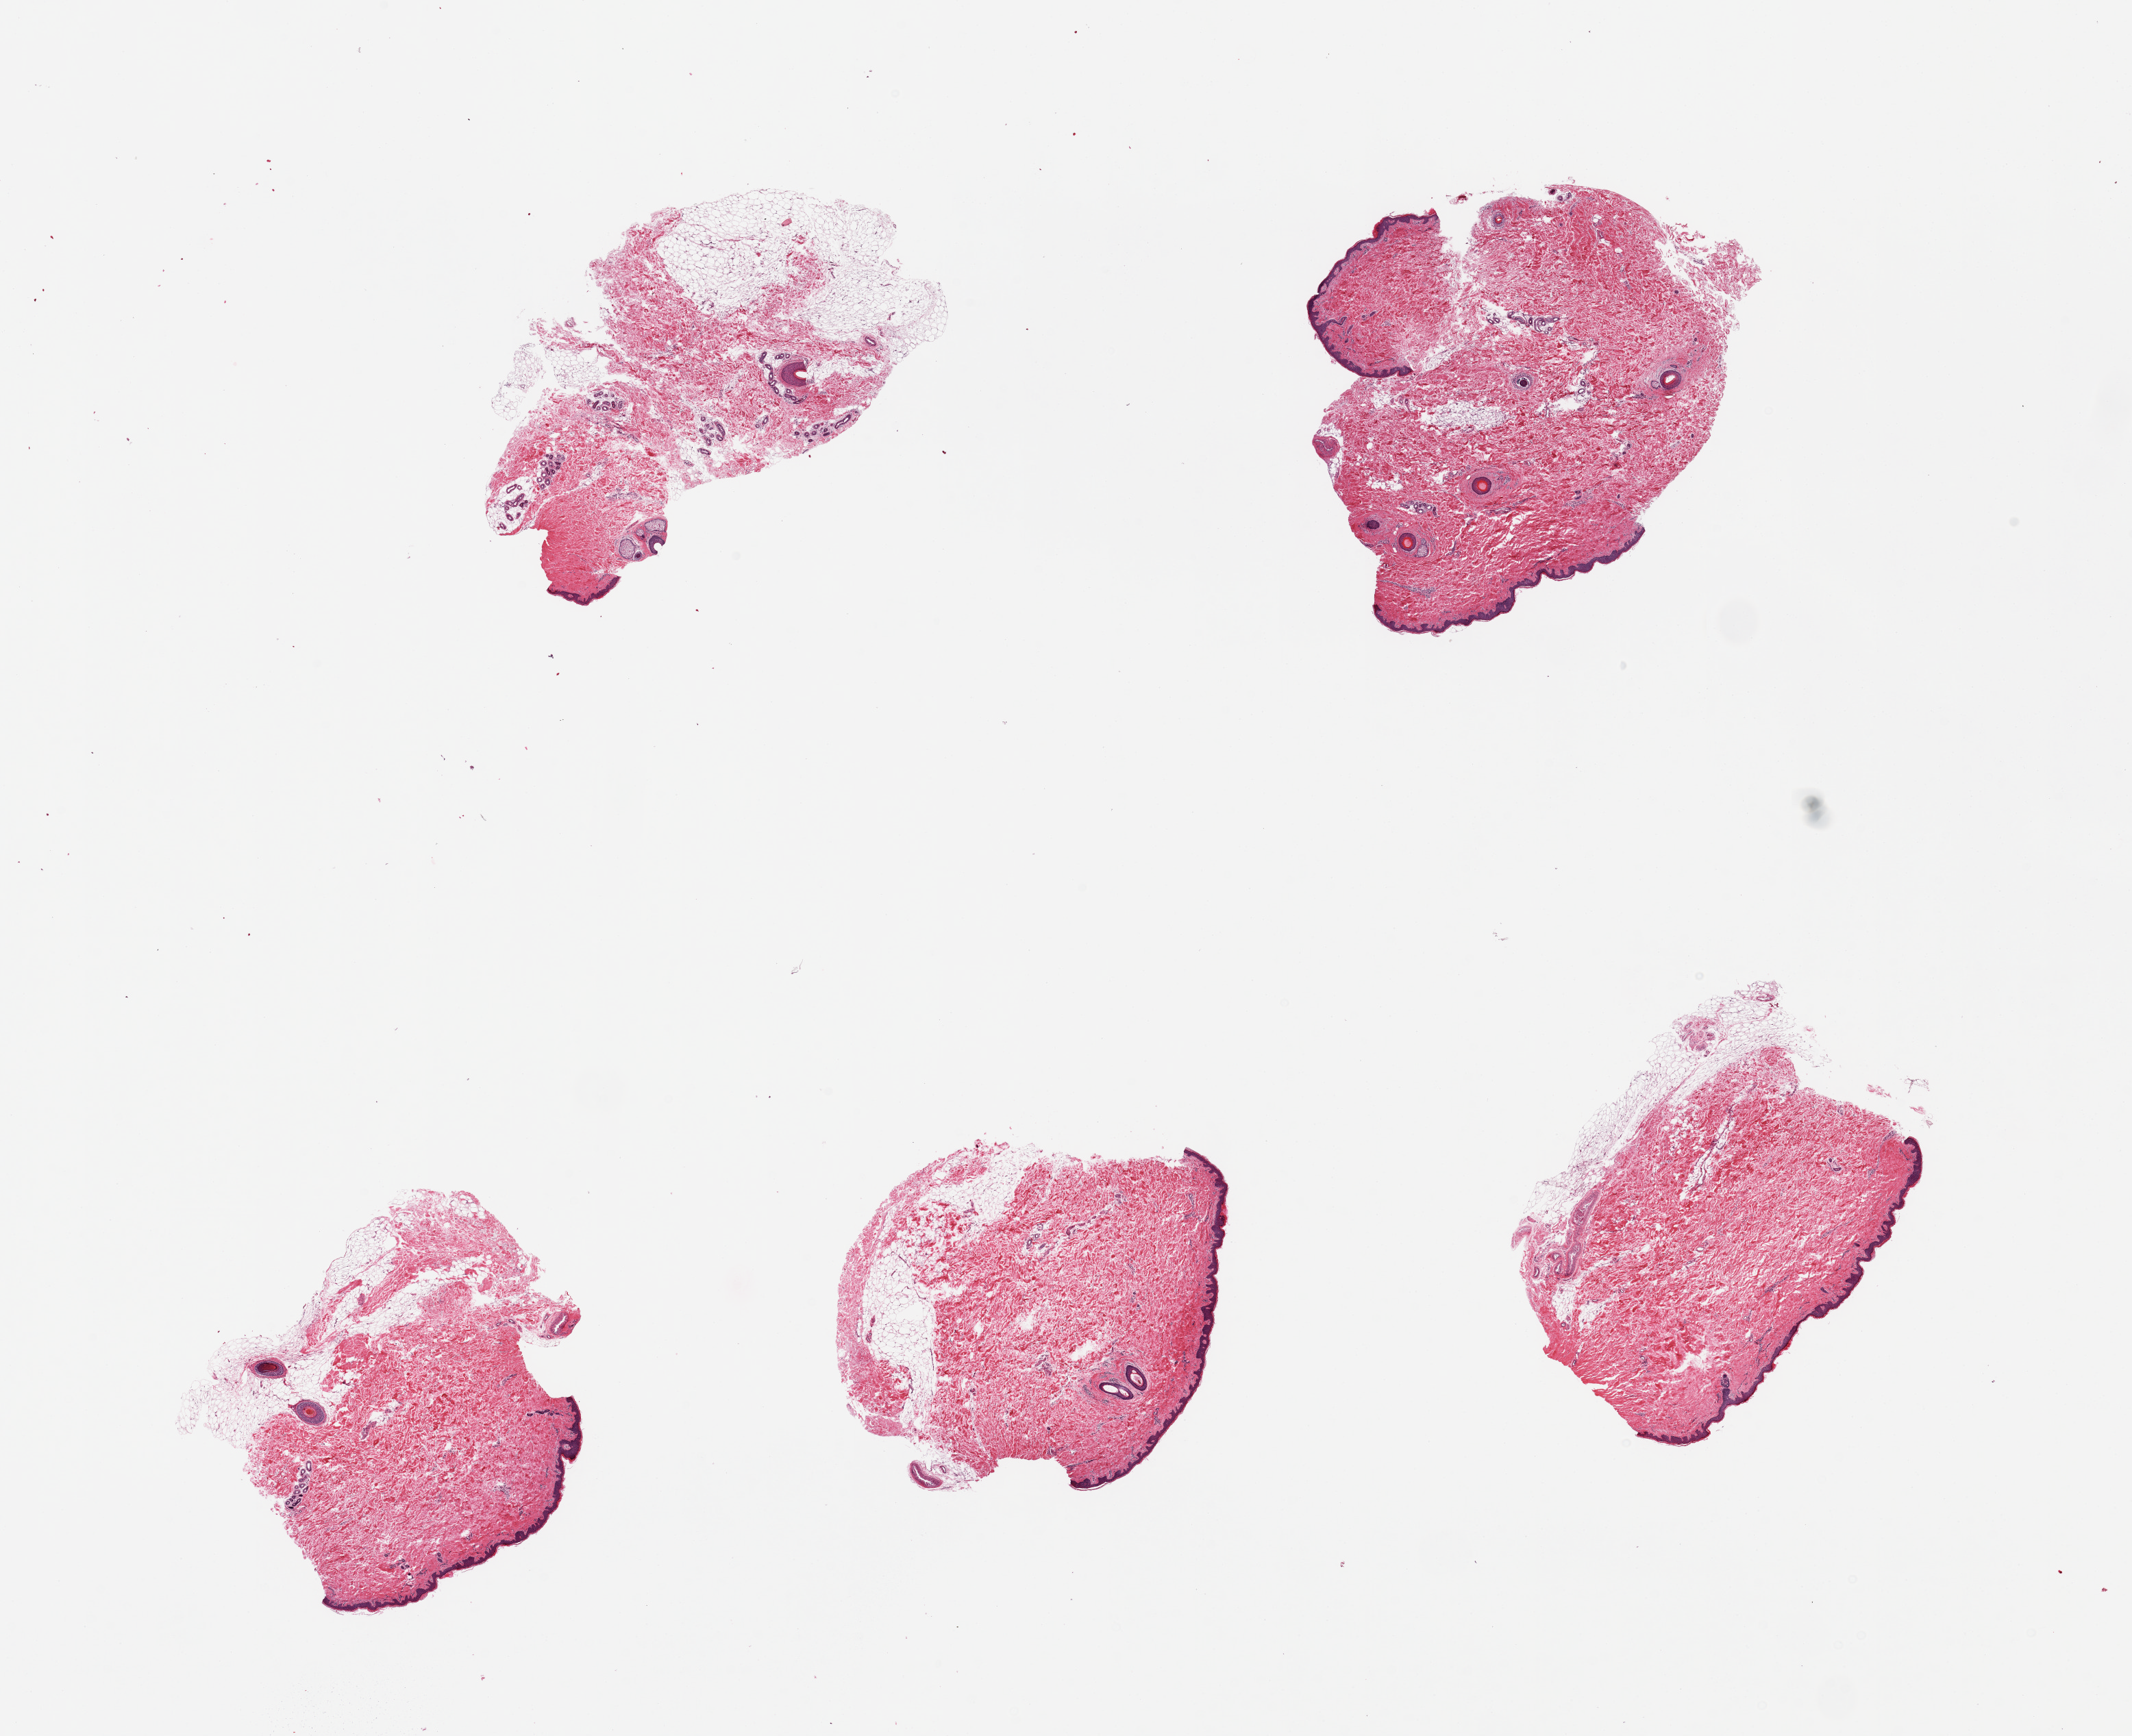
Whole-slide image, haematoxylin and eosin stain — whole scanned area (about 24.6 x 20.0 mm) shown as a low-resolution overview; PAXgene-fixed, paraffin-embedded tissue; target tissue: skin of suprapubic region; tissue donor sample. Donor: male.
• reviewer comment on this tissue sample: 5 pieces, trace dermal fat on several